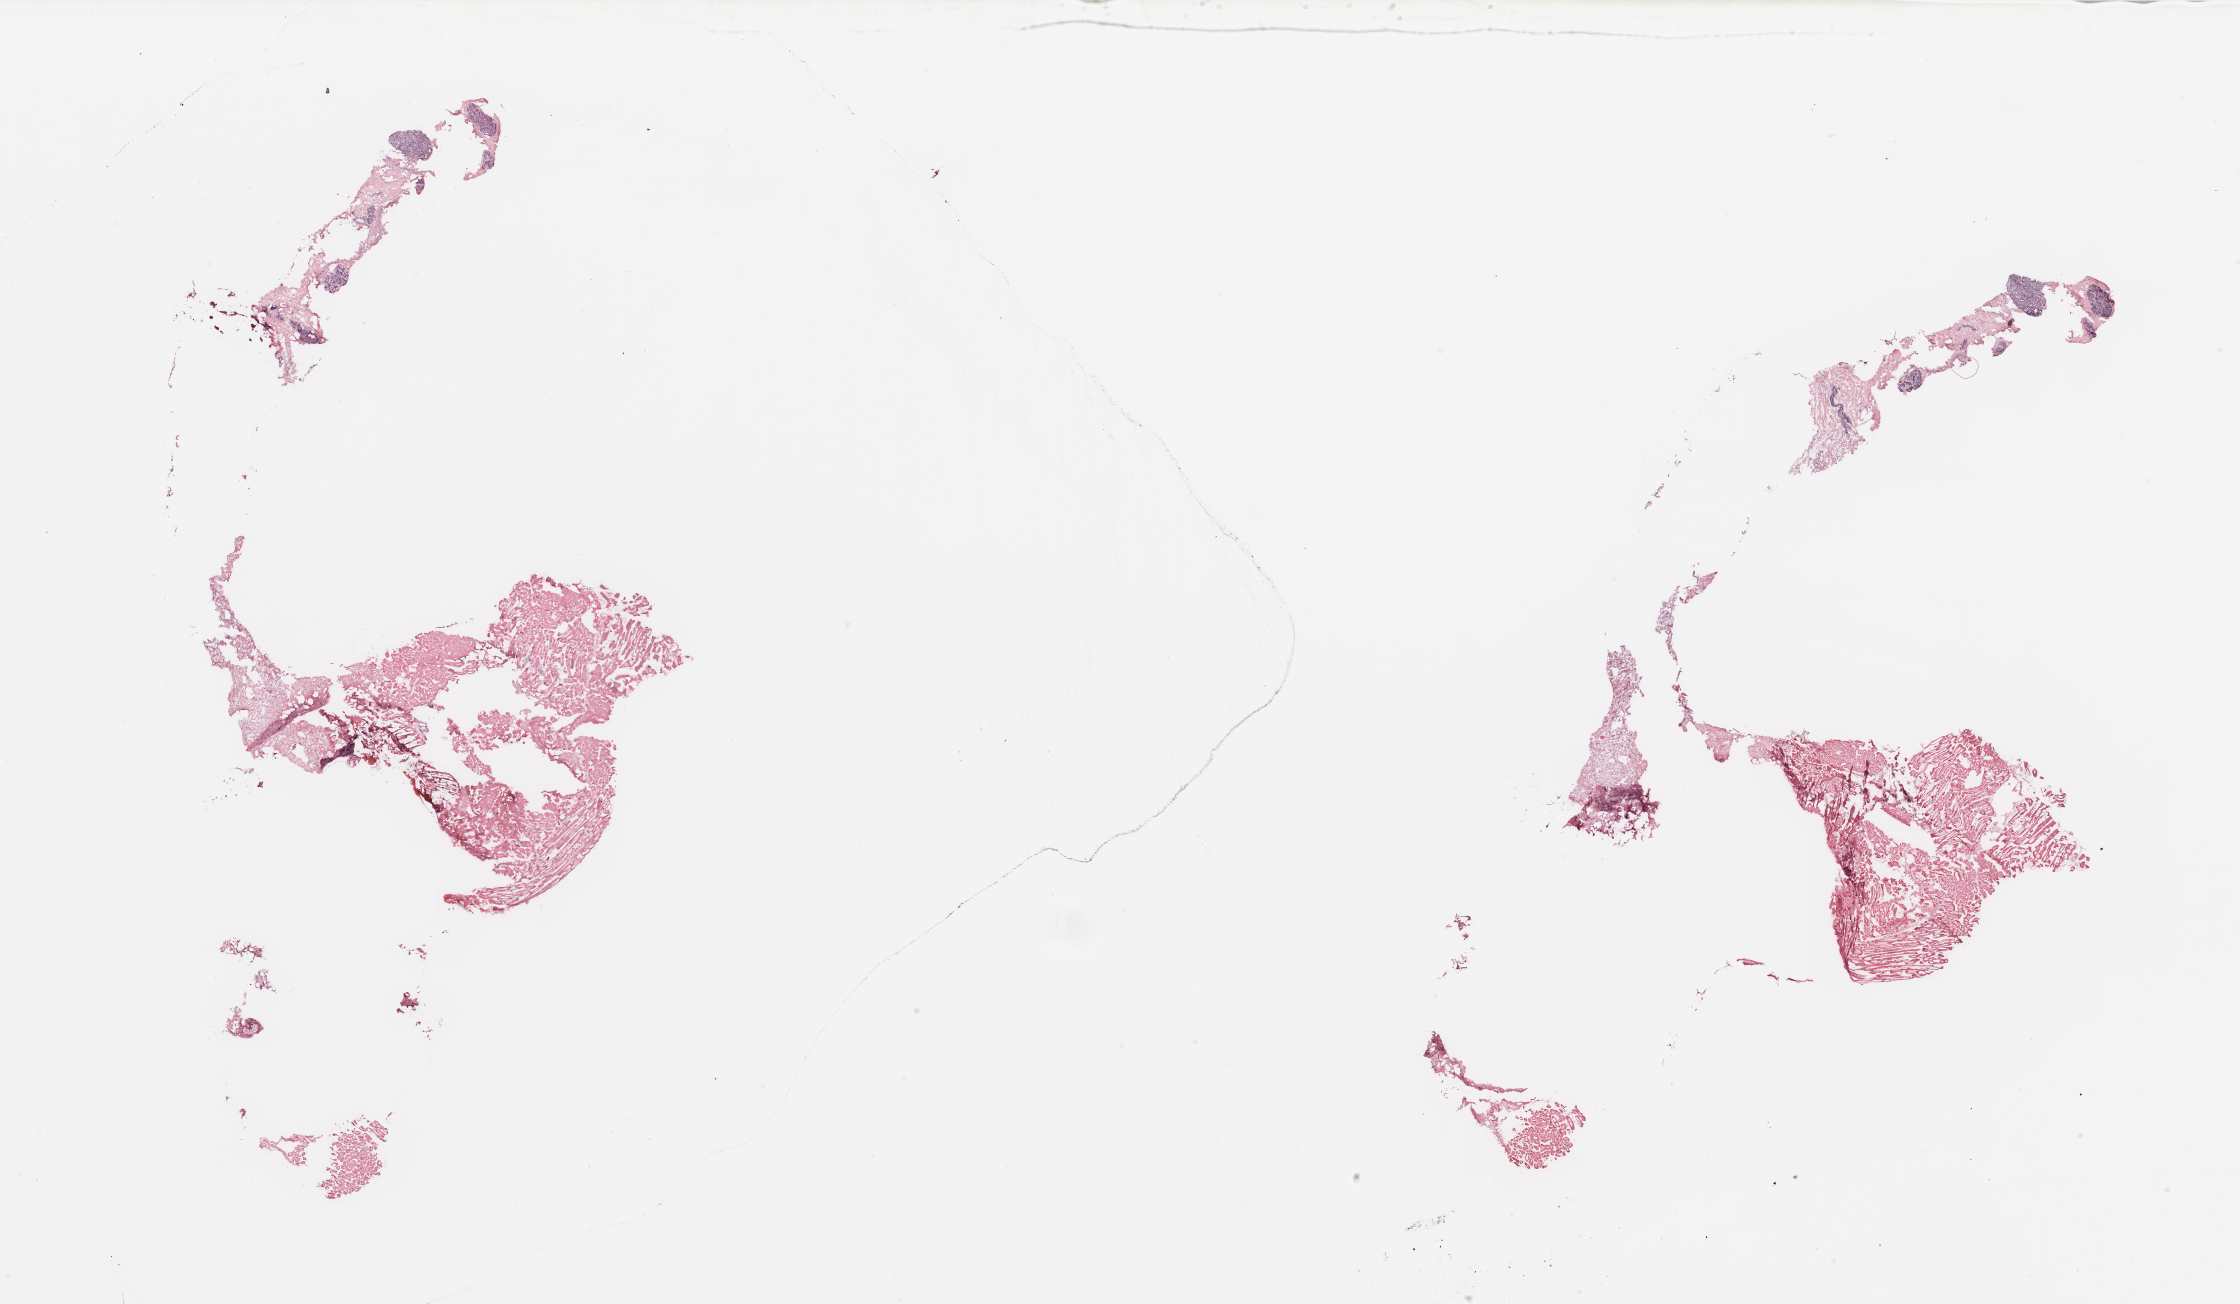
Digitized H&E-stained tissue section (whole slide) — whole scanned area (about 35.4 x 20.6 mm, acquisition: 20x scan) shown as a low-resolution overview. Breast, tissue type not recorded.
Patient diagnosis (cohort enrolment): breast cancer (breast).